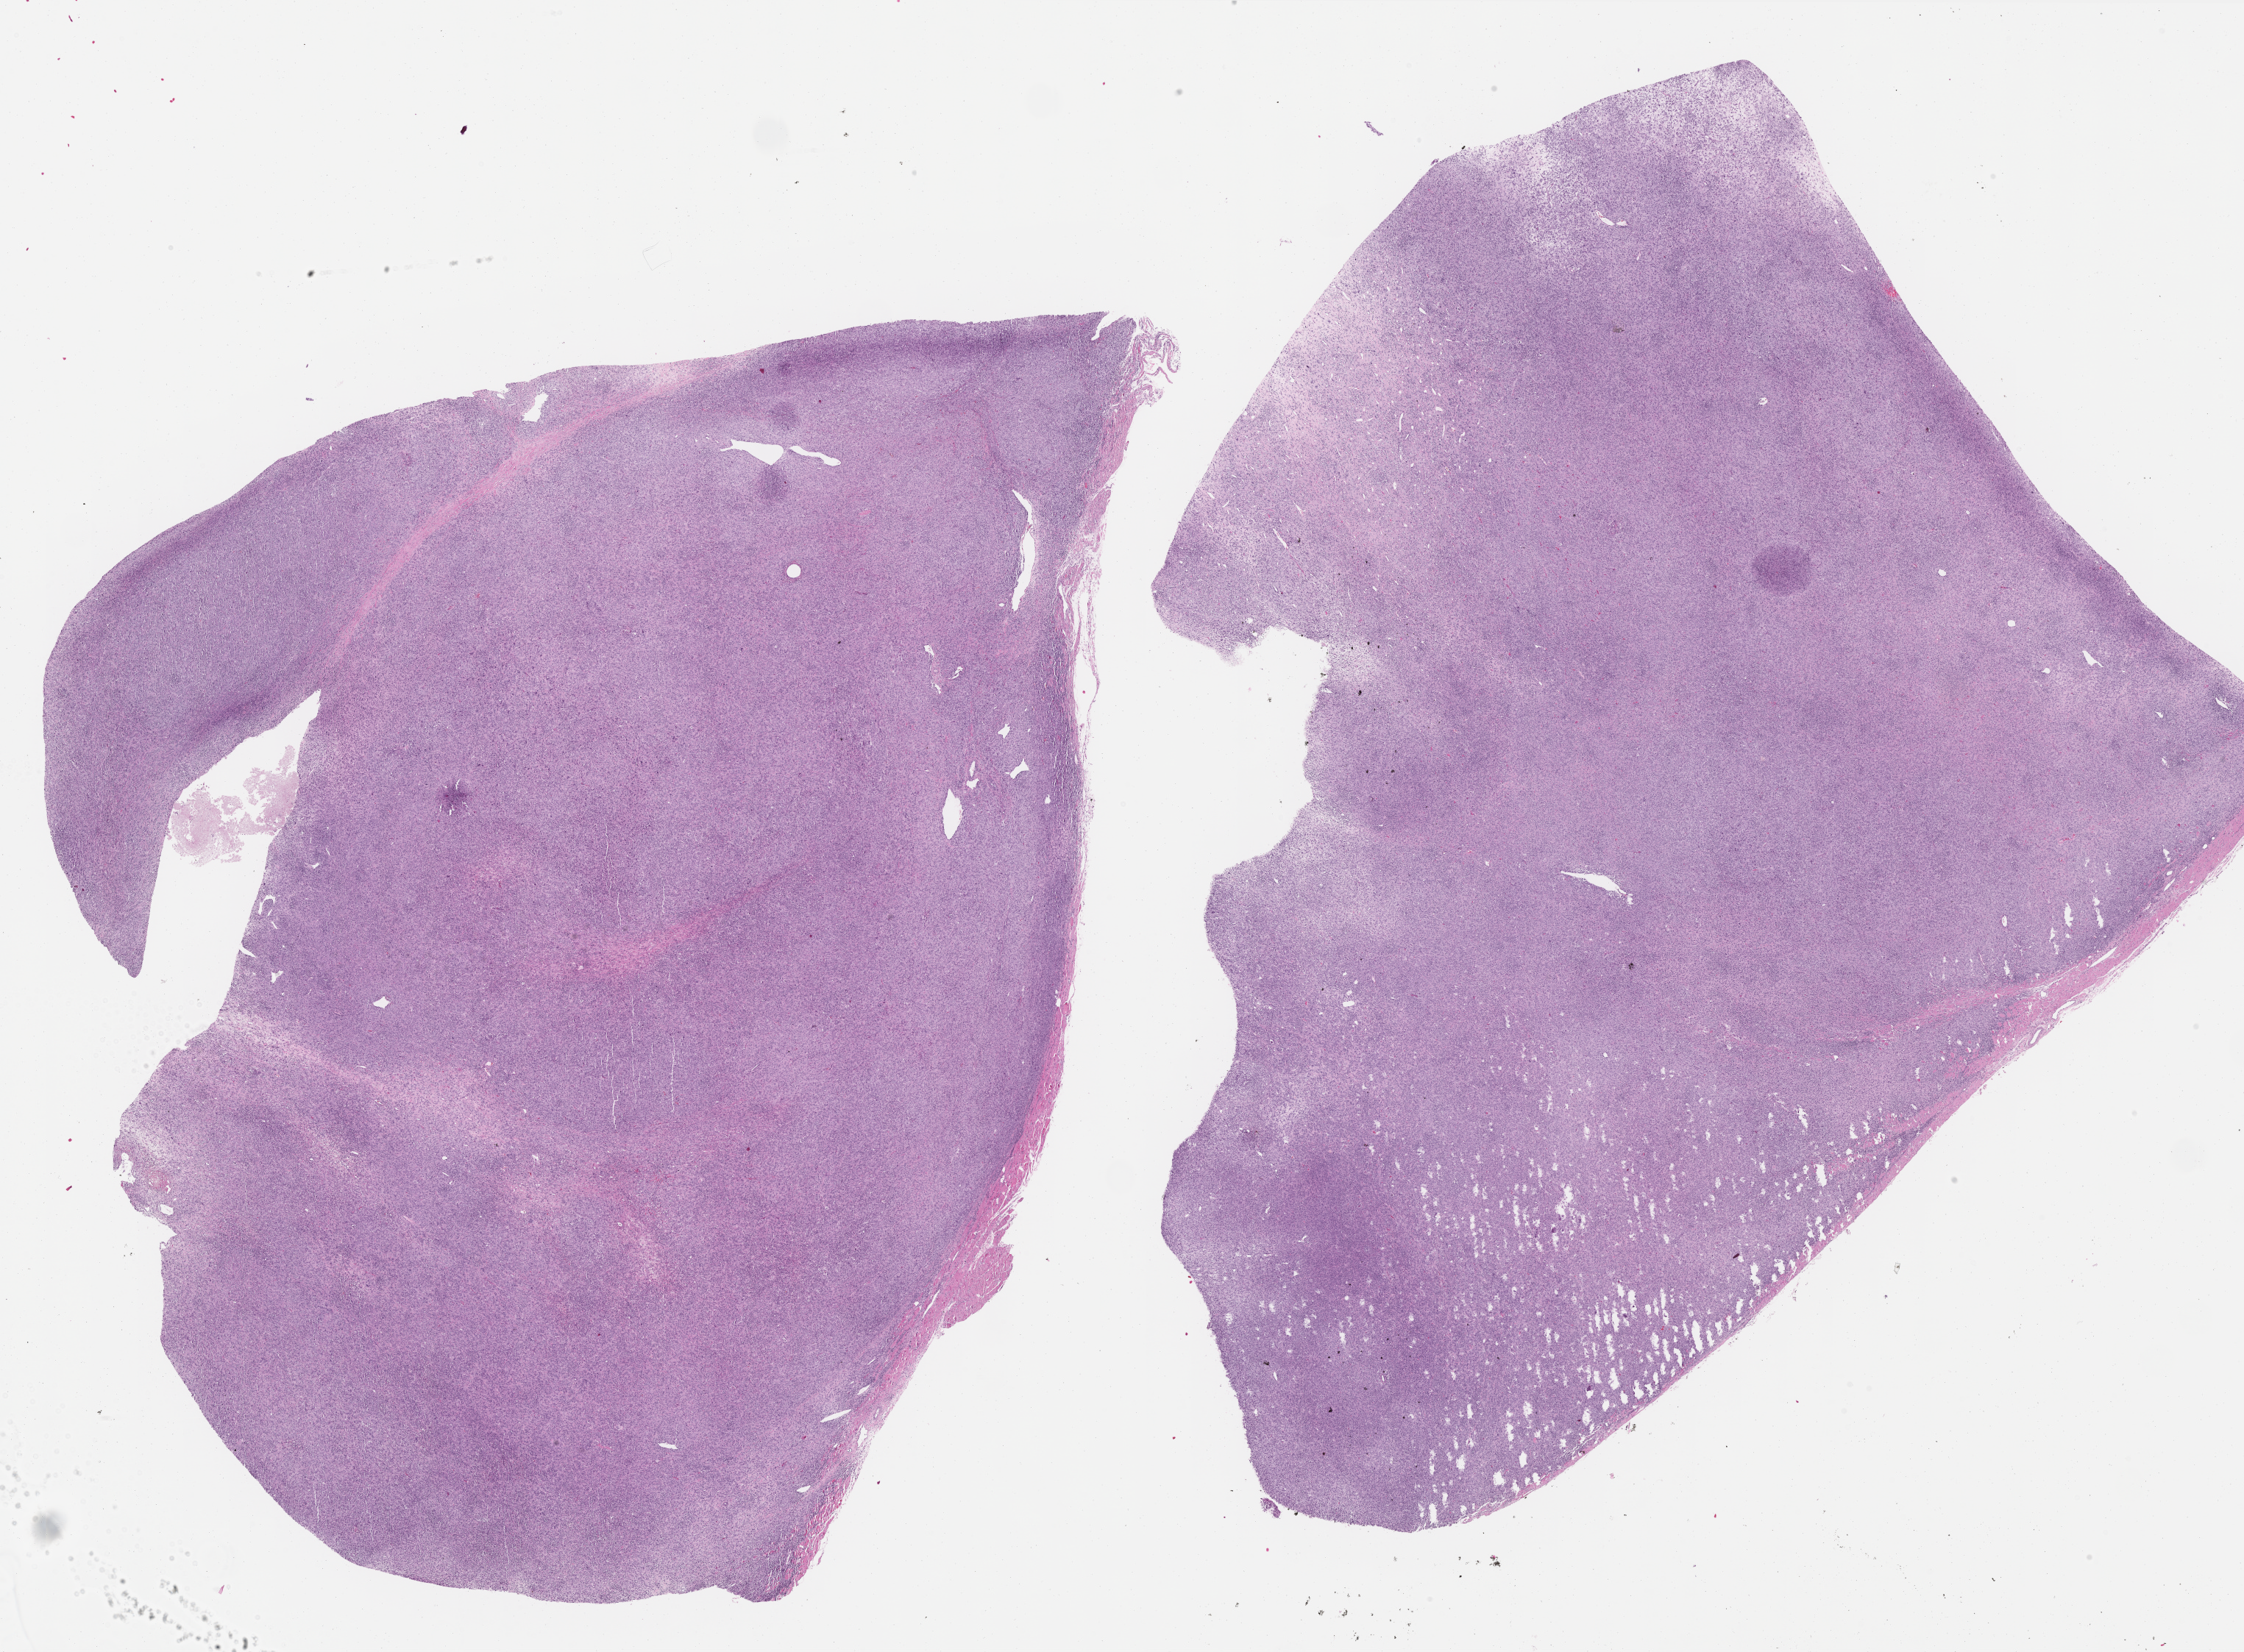
H&E whole-slide image, a low-resolution overview of the entire scanned area, about 24.5 x 18.1 mm (slide scanned at 40x); formalin-fixed paraffin-embedded (FFPE) diagnostic section; sample: primary tumour, connective, subcutaneous and other soft tissues. Patient: male, age at initial diagnosis 85 years.
Diagnosis: Malignant fibrous histiocytoma (connective, subcutaneous and other soft tissues of lower limb and hip).